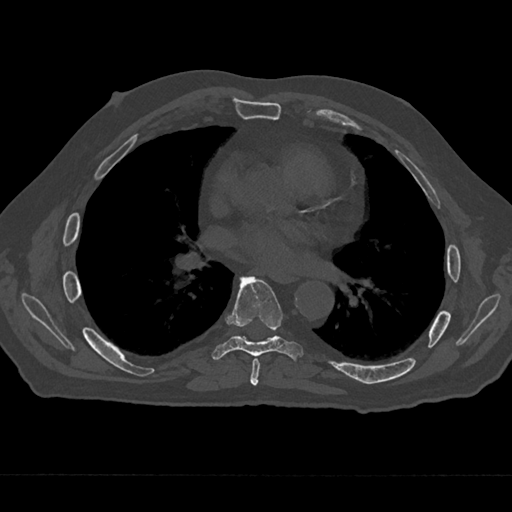
CT including the spine, one axial slice; position 373 of 797 along the scan axis; 120 kVp; bone window (W 1800 / L 400 HU); 0.5 mm slice thickness; 512 × 512 image matrix, field of view 377 × 377 mm. Patient: male, 75 years. From the clinical record (not read from this slice): primary cancer: renal; vertebrae with lytic lesions (as recorded): T4.
Annotated regions visible in this slice (semi-automatically segmented with operator editing):
- T6 vertebra: box from (x=250, y=358) to (x=260, y=386) px
- T7 vertebra: (x=211, y=276)–(x=303, y=361)